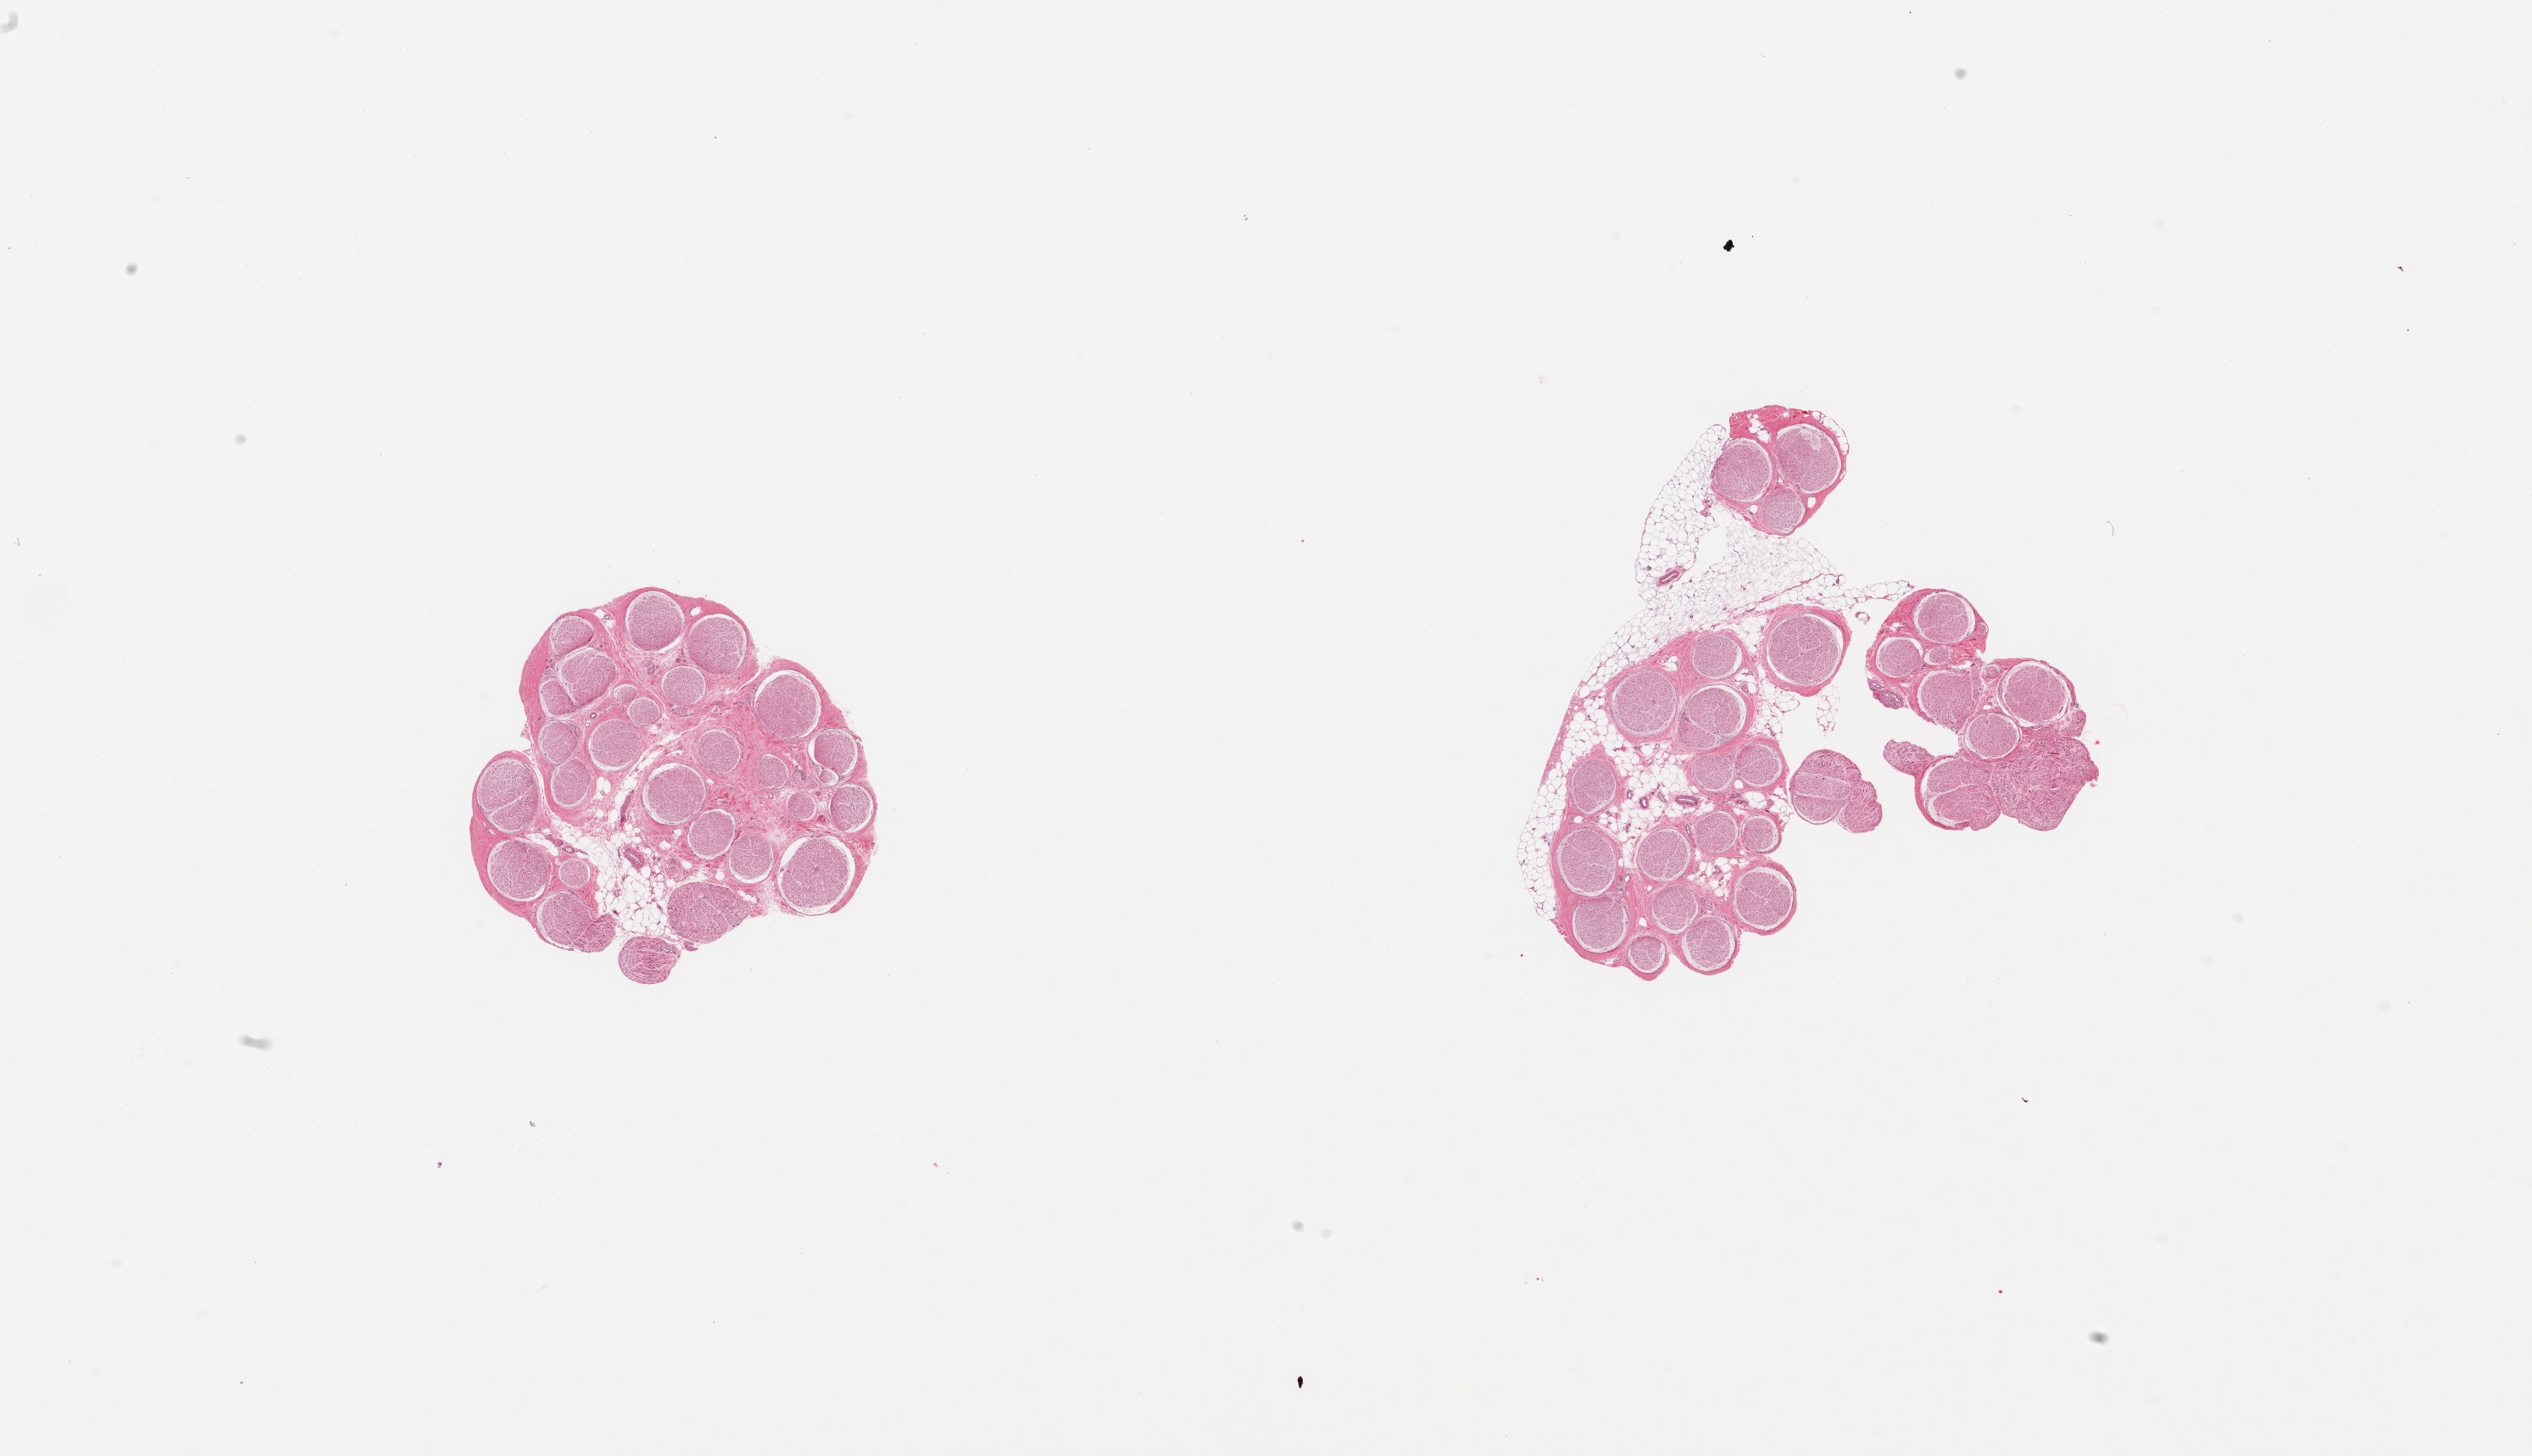
Digitized H&E-stained section, whole scanned area (about 23.6 x 13.6 mm) shown as a low-resolution overview. PAXgene-fixed paraffin-embedded (PFPE) section. Sampled site (target tissue): tibial nerve. Donor tissue sample. Donor: male.
* pathologist's review note for this sample: 2 pieces; interstitial fat is ~10% of tissue